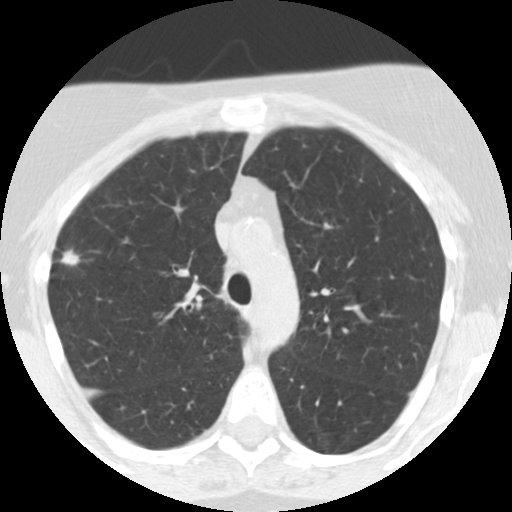
Low-dose screening chest CT, one axial slice; slice 179 of 248 in the series (ordered by position); reconstruction kernel STANDARD; lung window (W 1500 / L -600 HU); 2.5 mm slice thickness; 512 × 512 image matrix, field of view 287 × 287 mm.
Outlined on this slice (expert manual segmentation):
- lesion 1 (tumor, upper lobe of right lung): bounding box <61,251,79,265> (left, top, right, bottom; pixels)